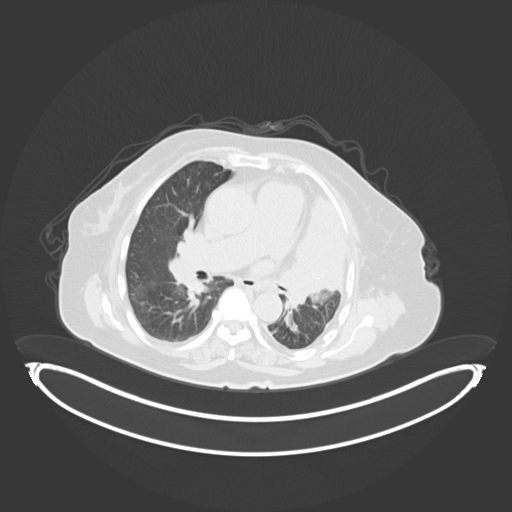
Chest CT, one axial slice; position 199 of 284 along the scan axis; lung window (W 1500 / L -600 HU); 512 × 512 image matrix. Female patient, age 75 years. From the clinical record (not read from this slice): clinical TNM (as recorded): T3 N3 M1.
Outlined on this slice (rectangle marked by the reading radiologist):
- lung tumour (recorded histology: adenocarcinoma): bounding box <277,187,352,311> (left, top, right, bottom; pixels)